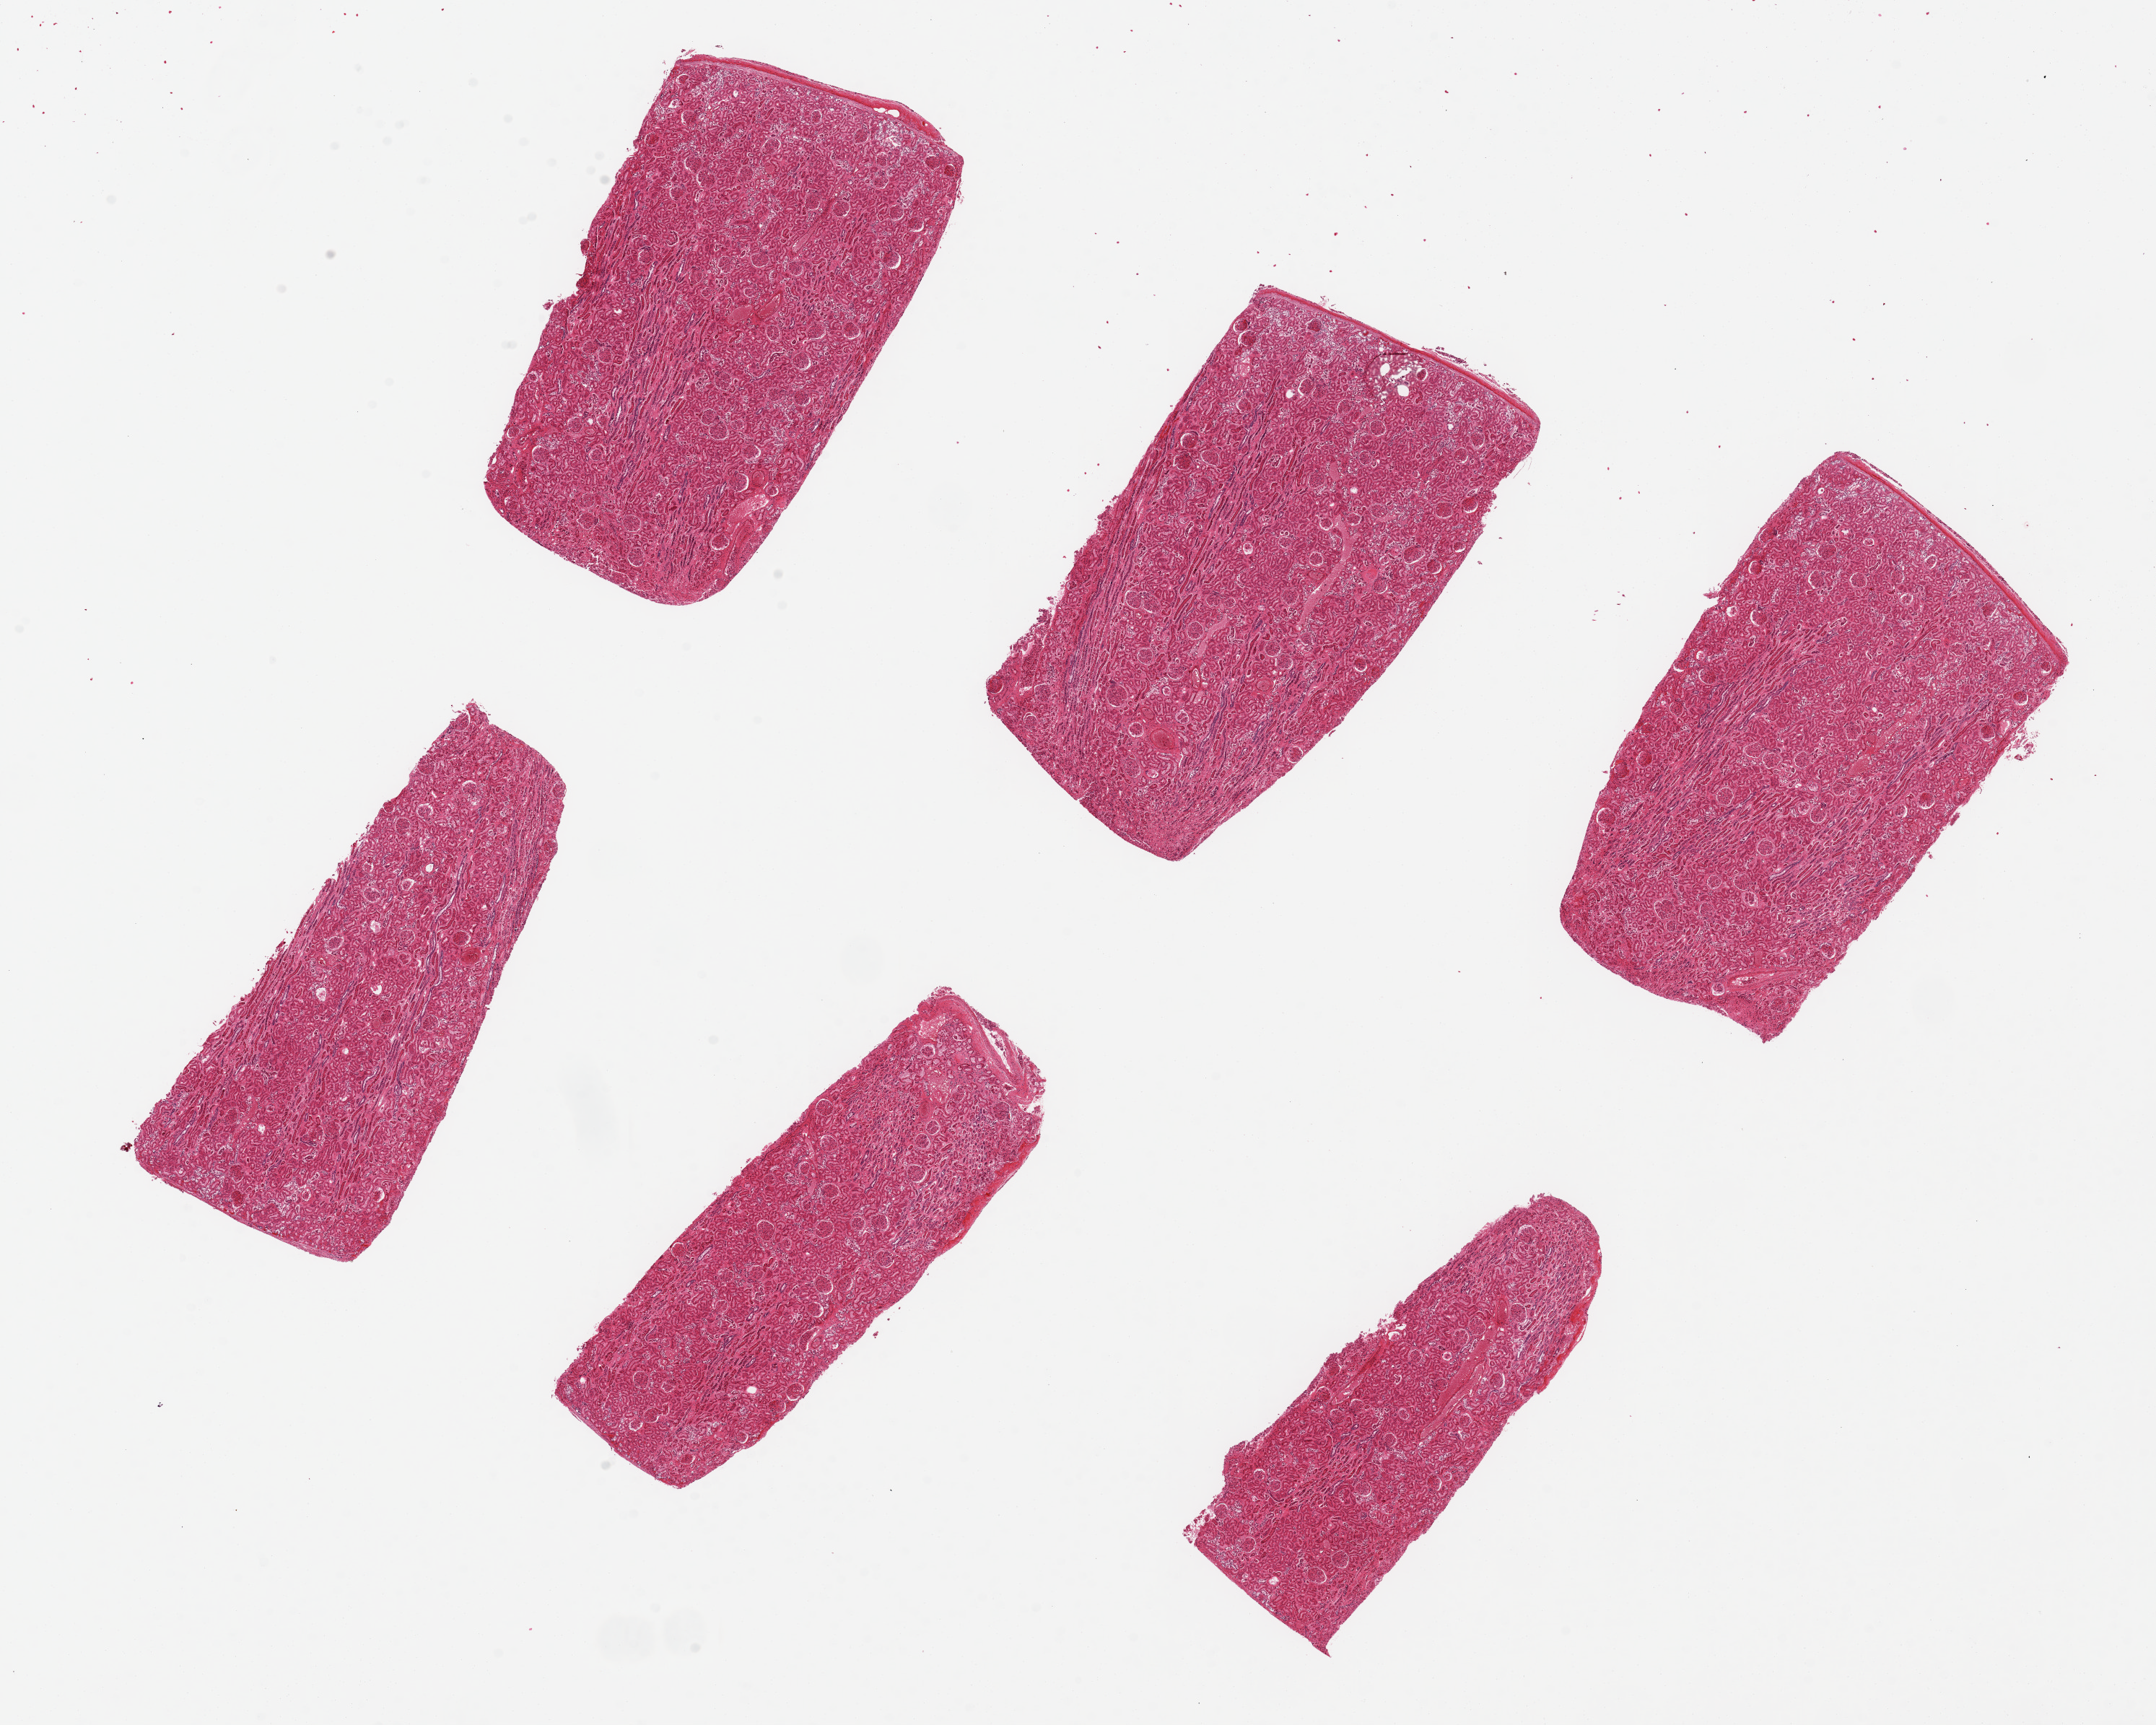
Whole-slide image, H&E stain, a low-resolution overview of the entire scanned area, about 23.6 x 18.9 mm, PAXgene-fixed paraffin-embedded (PFPE) section, target tissue: renal cortex, tissue donor sample. Donor: male.
• pathologist's review note for this sample: 6 pieces up to 6x3 mm; all cortex; no underlying chronic renal lesions